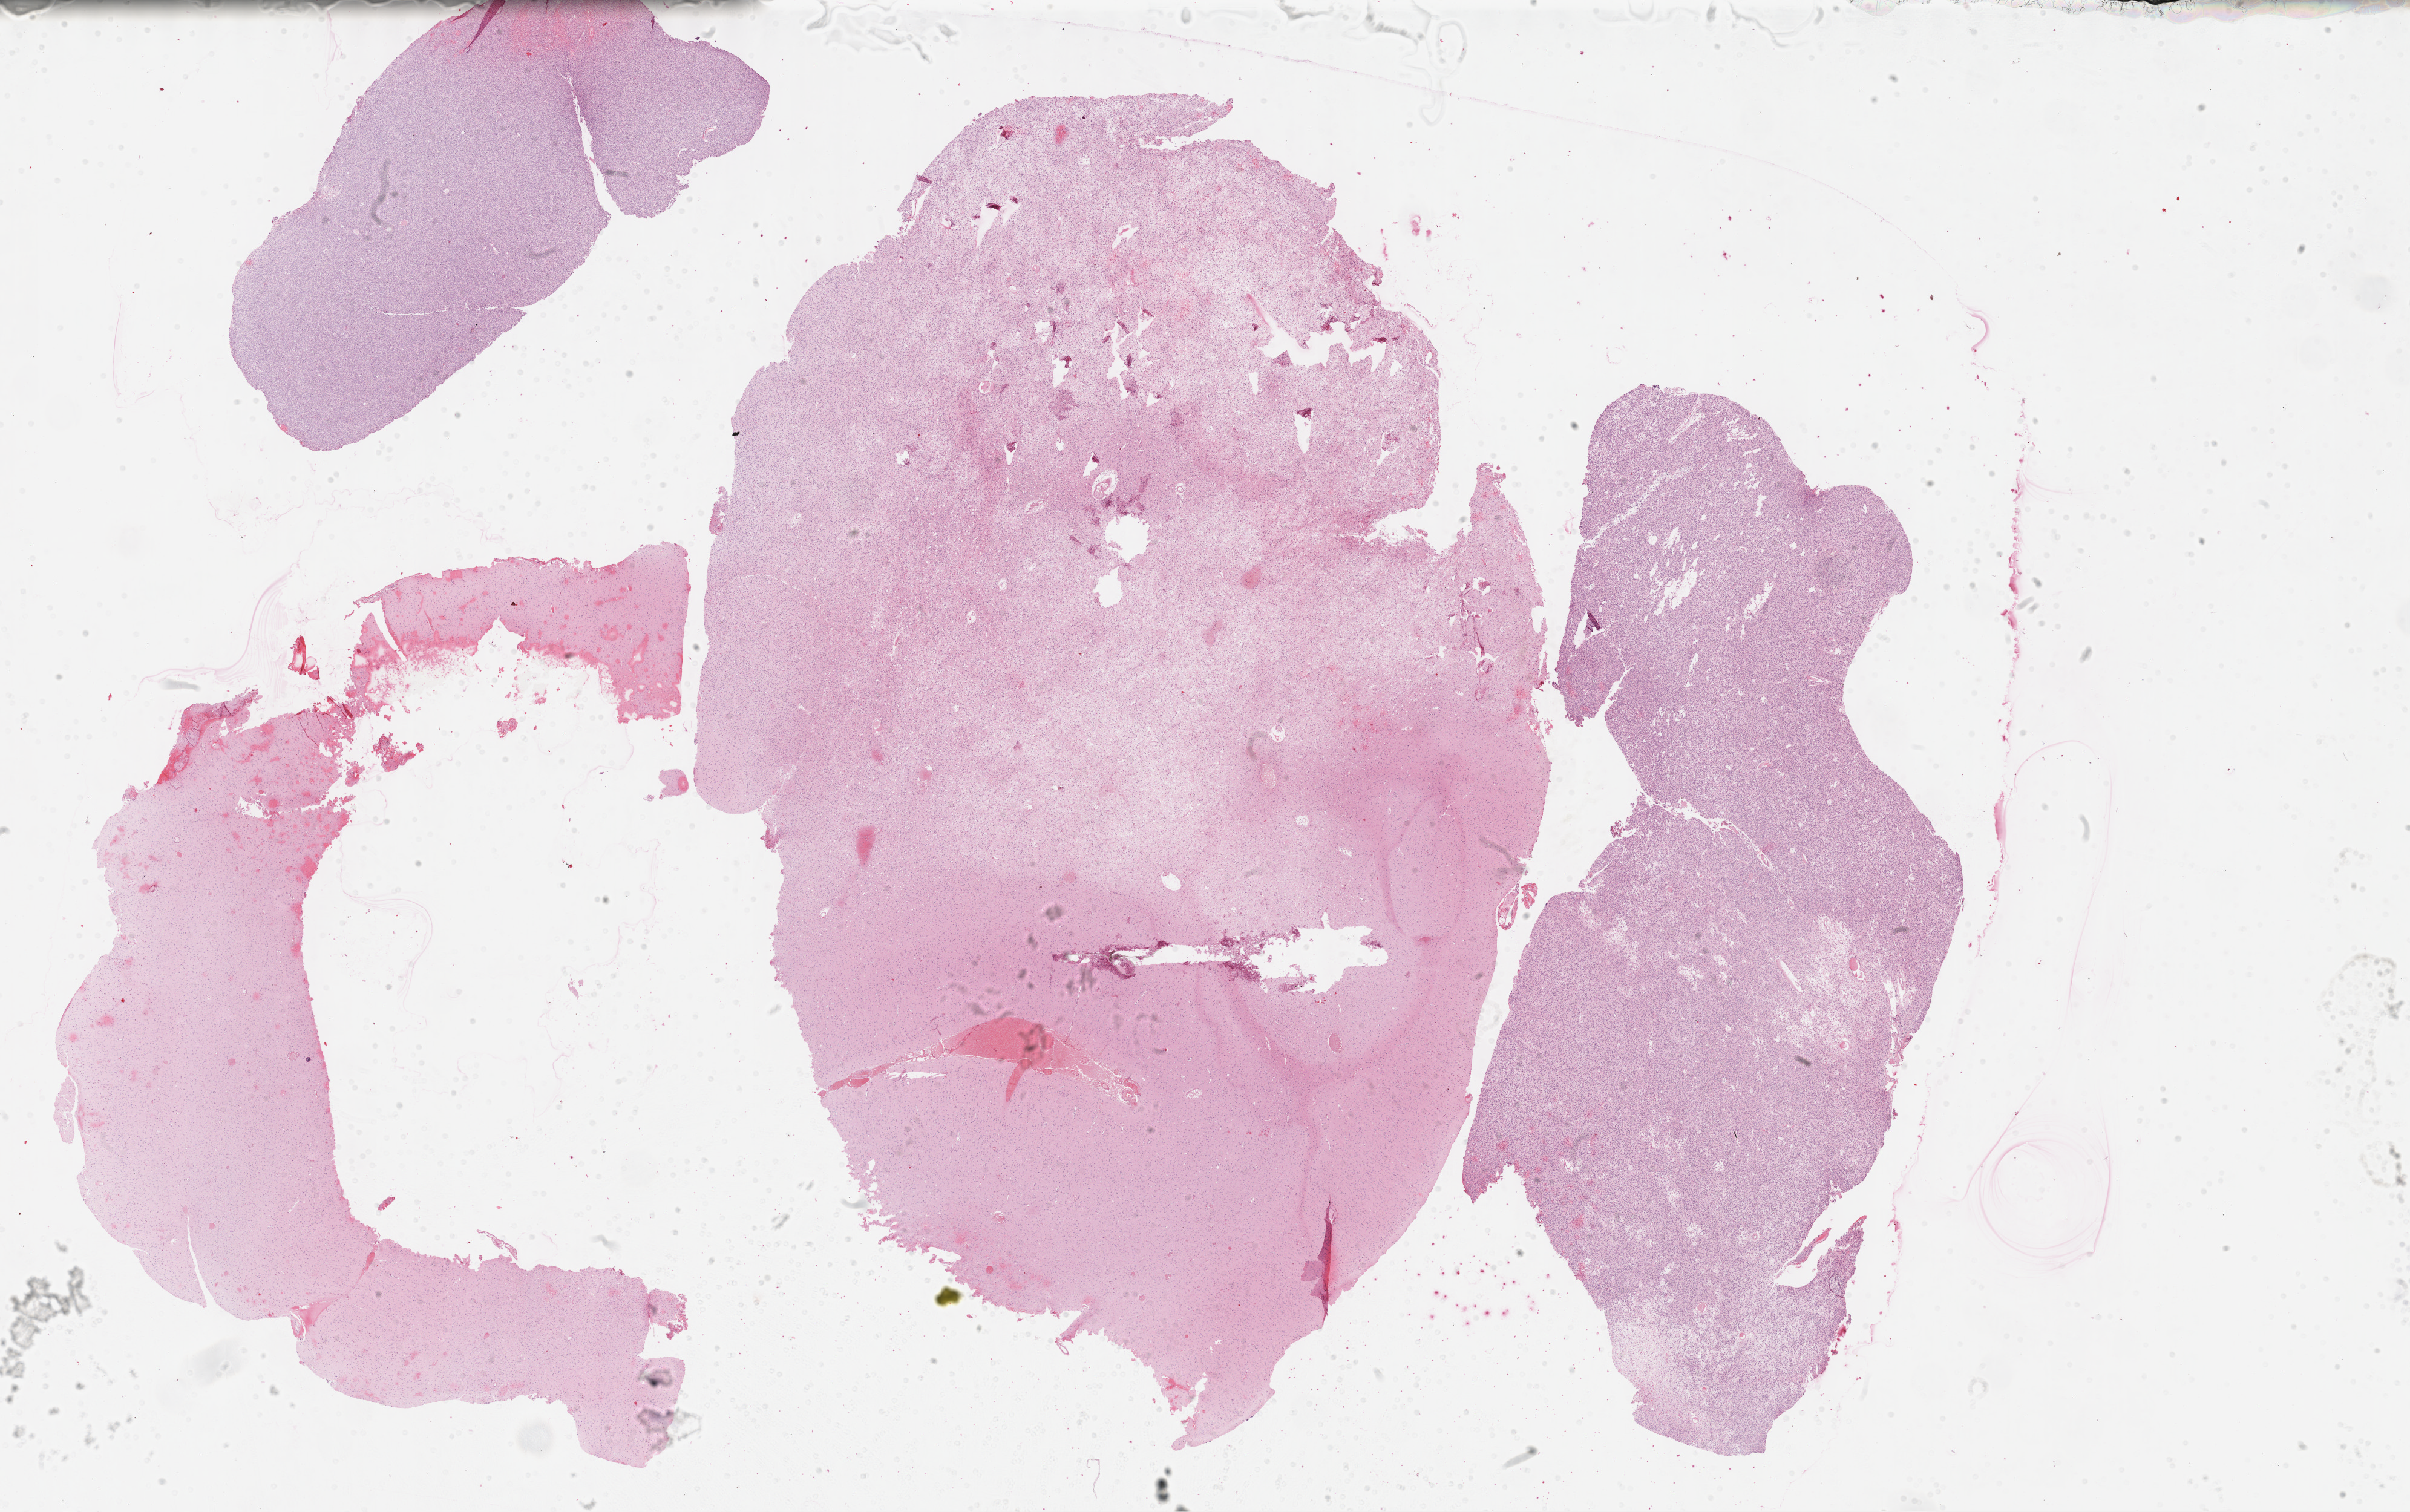
Digitized Hematoxylin and eosin (H&E) stained tissue section (whole slide) — a low-resolution overview of the entire scanned area, about 32.2 x 20.2 mm (from a 40x scan). FFPE section. Sample: primary tumour, brain. Patient: female, age at initial diagnosis 56 years. Histologic grade: G3 (poorly differentiated).
Pathologic diagnosis: Oligodendroglioma, anaplastic.